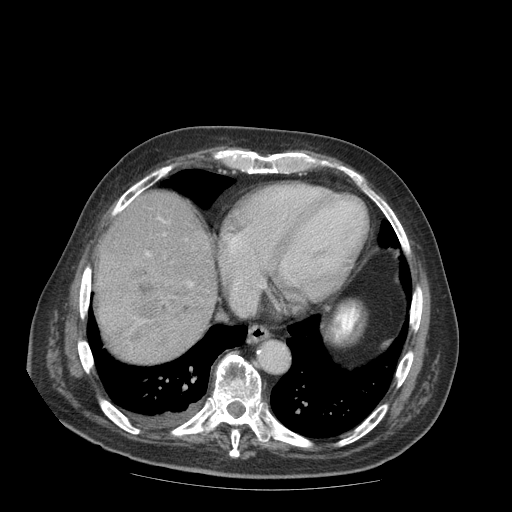
Contrast-enhanced abdominal CT (liver protocol), one axial slice. Position 81 of 99 along the scan axis. Reconstruction kernel STANDARD. Soft-tissue window (W 400 / L 40 HU). 2.5 mm slice thickness. 512 × 512 image matrix. From the clinical record (not read from this slice): diagnosis: hepatocellular carcinoma (patient treated with transarterial chemoembolisation; whether this scan precedes or follows treatment is not stated here); TNM stage (as recorded): Stage-IIIB; Child-Pugh class: A; tumour differentiation: well differentiated.
Structures marked on this image (semi-automatically segmented with operator editing):
- liver parenchyma outside the tumour (the mass and vessels are separate outlines, so this box may not span the whole liver): box from (x=94, y=192) to (x=216, y=317) px
- mass: (x=95, y=254)–(x=214, y=365)
- liver vessels: (x=146, y=218)–(x=165, y=257)